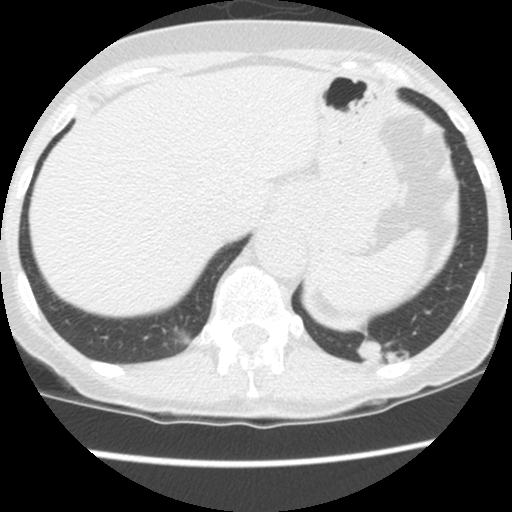
Low-dose screening chest CT, one axial slice. Position 23 of 130 along the scan axis. Reconstruction kernel STANDARD. 120 kVp. Lung window (W 1500 / L -600 HU). 2.5 mm slice thickness. 512 × 512 image matrix, field of view 290 × 290 mm.
Annotated regions visible in this slice (manually delineated by an expert):
- lesion 1 (tumor, lower lobe of left lung): box from (x=356, y=336) to (x=410, y=365) px